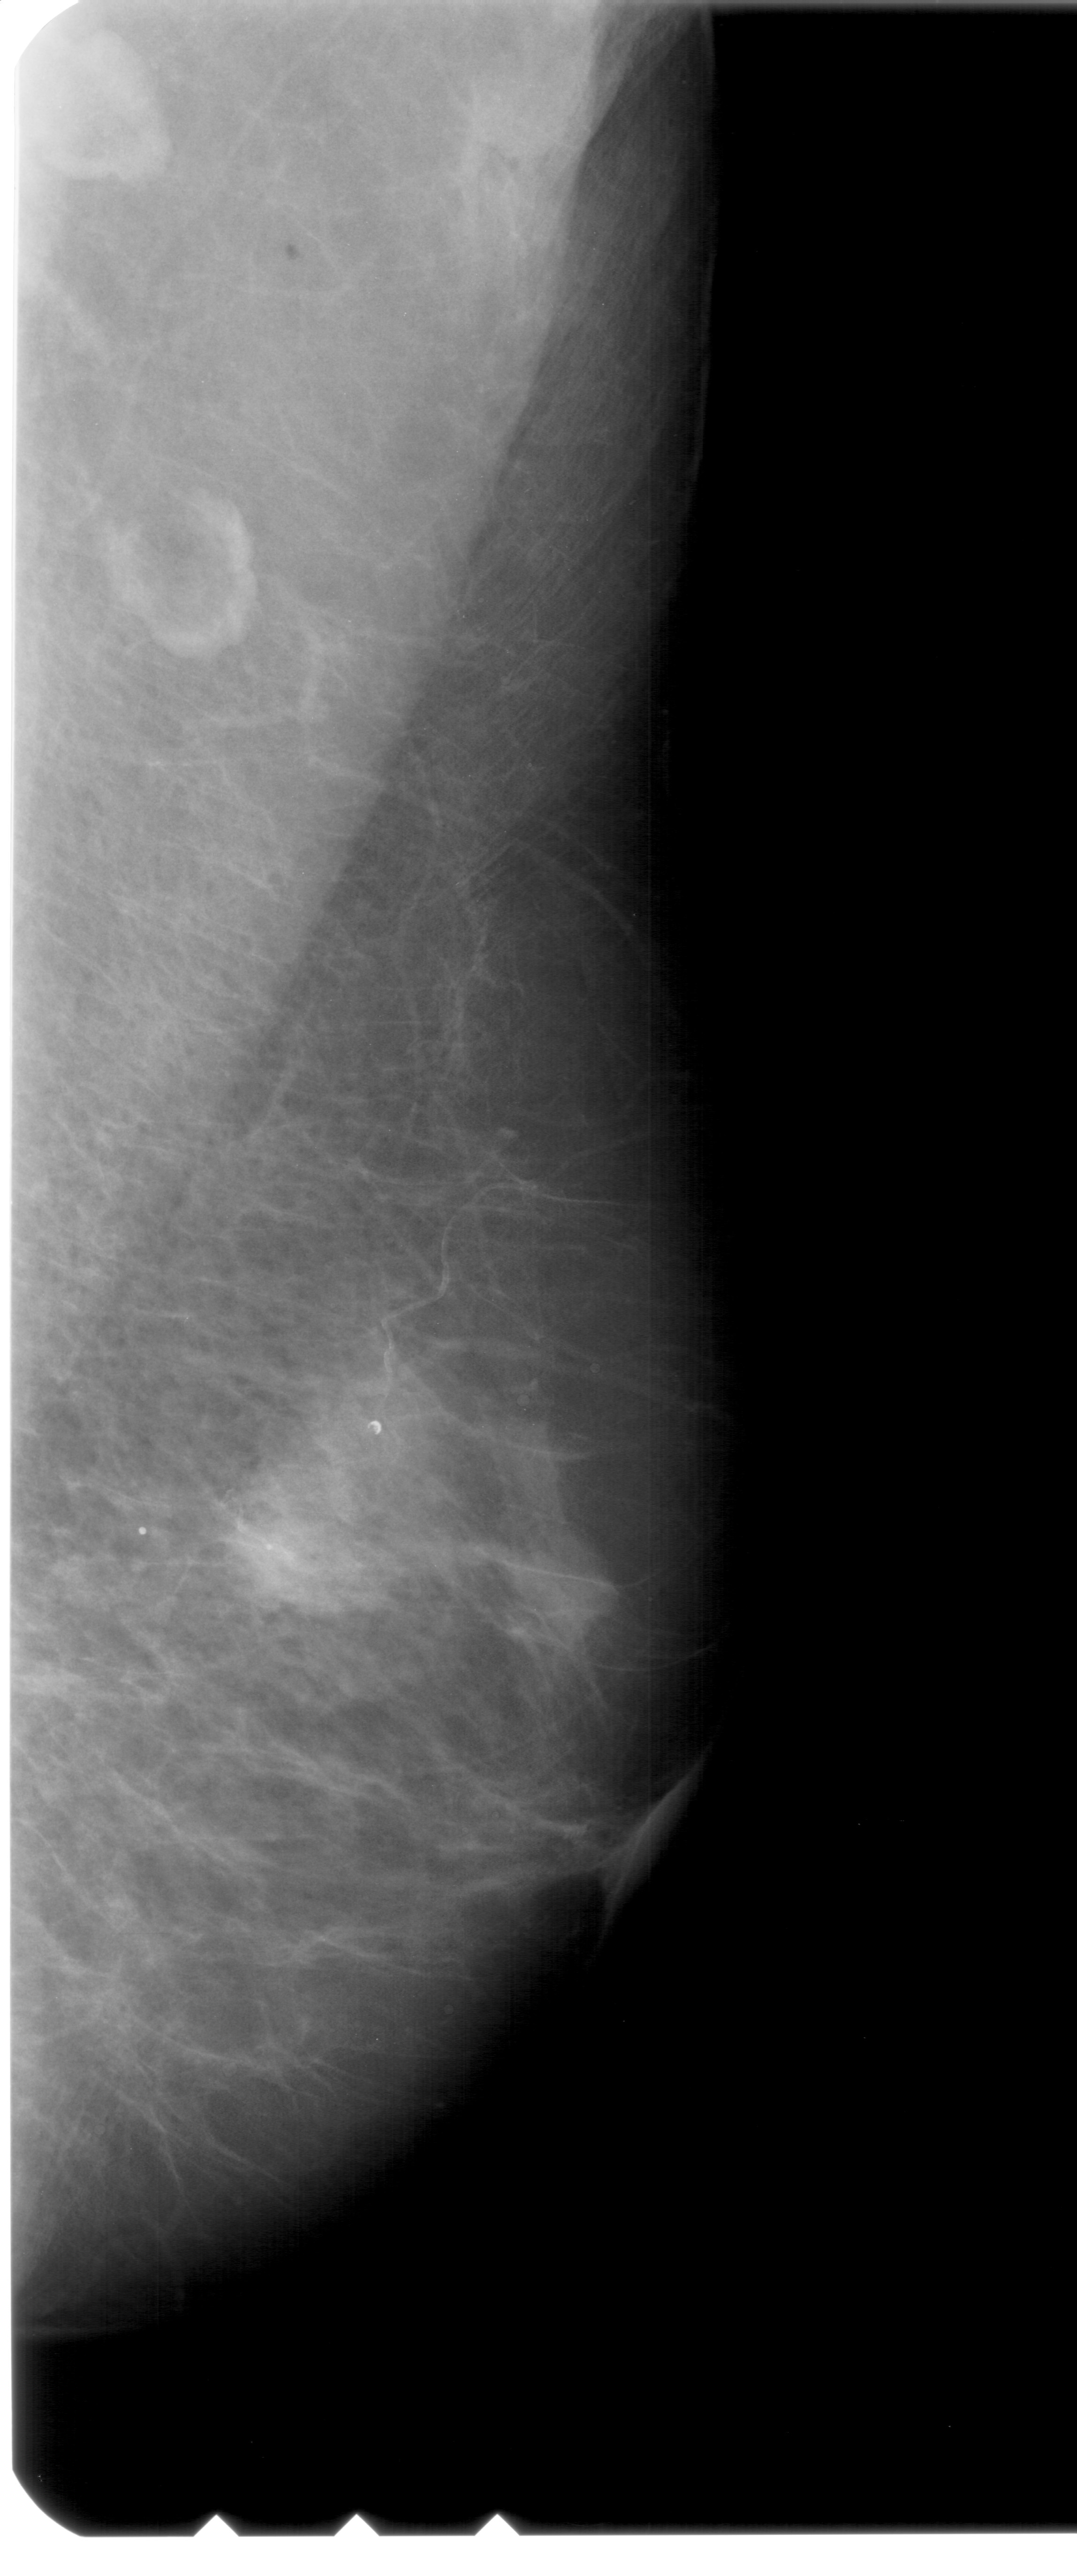
Digitized screen-film mammogram; right breast; MLO view; BI-RADS breast density category 2 (scale 1–4).
- Marked findings (only marked abnormalities are described; nothing is implied about the rest of the image): Finding 1 of 2: mass, shape oval, margins ill defined; BI-RADS assessment category 4; pathology (as recorded): malignant.
- Finding 2 of 2: mass, shape oval, margins ill defined; BI-RADS assessment category 4; subtlety rating 4 on a 1 (subtle) to 5 (obvious) scale; pathology result (as recorded, not read from the image): malignant.